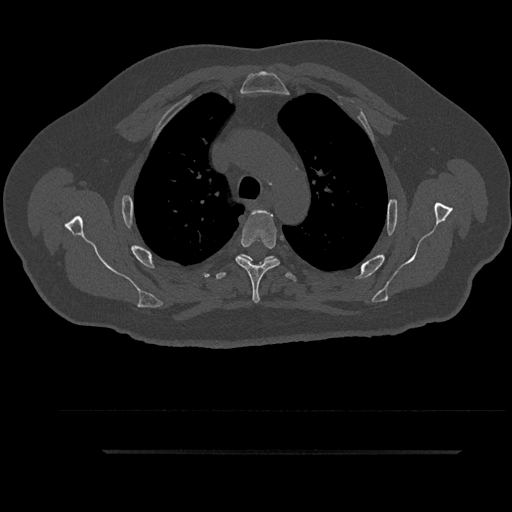
CT including the spine, one axial slice. Position 667 of 797 along the scan axis. Reconstruction kernel Br40s/3. 120 kVp. Bone window (W 1800 / L 400 HU). 0.5 mm slice thickness. 512 × 512 image matrix, field of view 432 × 432 mm. Male patient, age 63 years. Case-level facts recorded for this patient, not image findings: primary cancer: renal.
Outlined on this slice (semi-automatically segmented with operator editing):
- T4 vertebra: box from (x=235, y=209) to (x=280, y=303) px
- T5 vertebra: (x=256, y=257)–(x=269, y=266)